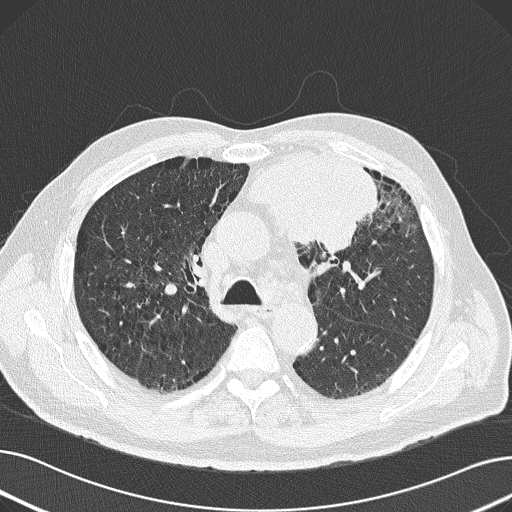
Axial slice from a low-dose chest CT screening exam; baseline annual screen; lung window (W 1500 / L -600 HU); 2 mm slice thickness; lung (sharp) reconstruction kernel (B50f); slice 64 of 165 in the series; 512 × 512 image matrix, field of view 370 × 370 mm. Male participant, aged 69 years at enrolment. Former smoker at enrolment.
Expert reader's lesion annotation, bounding box [x1, y1, x2, y2] px = [230, 141, 381, 252]. Reader record for this screening exam (exam-level; its link to the box is not recorded): non-calcified nodule or mass ≥4 mm, left upper lobe, 6 × 10 mm, spiculated (stellate) margins, soft tissue attenuation. Official screen result: positive, change unspecified: nodule(s) >= 4 mm or enlarging nodule(s), mass(es), or other non-specific abnormalities suspicious for lung cancer. Participant outcome: lung cancer diagnosed 20 days after this screen — non-small cell carcinoma, left upper lobe, poorly differentiated (G3), stage IB (AJCC 6th edition), 100 mm at pathology.